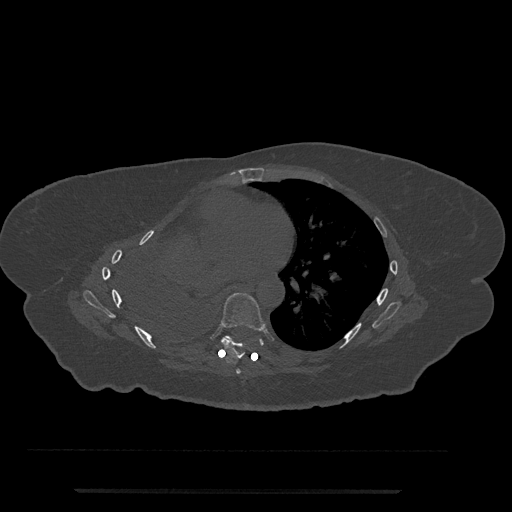
CT including the spine, one axial slice. Position 433 of 797 along the scan axis. 120 kVp. Bone window (W 1800 / L 400 HU). 512 × 512 image matrix, field of view 440 × 440 mm. Female patient, age 51 years. From the clinical record (not read from this slice): primary cancer: neuro; vertebrae with lytic lesions (as recorded): T8.
Annotated regions visible in this slice (semi-automatically segmented with operator editing):
- T6 vertebra: bounding box [x1, y1, x2, y2] px = [236, 369, 241, 374]
- T7 vertebra: [221, 293, 266, 359]
- T8 vertebra: [223, 336, 231, 339]